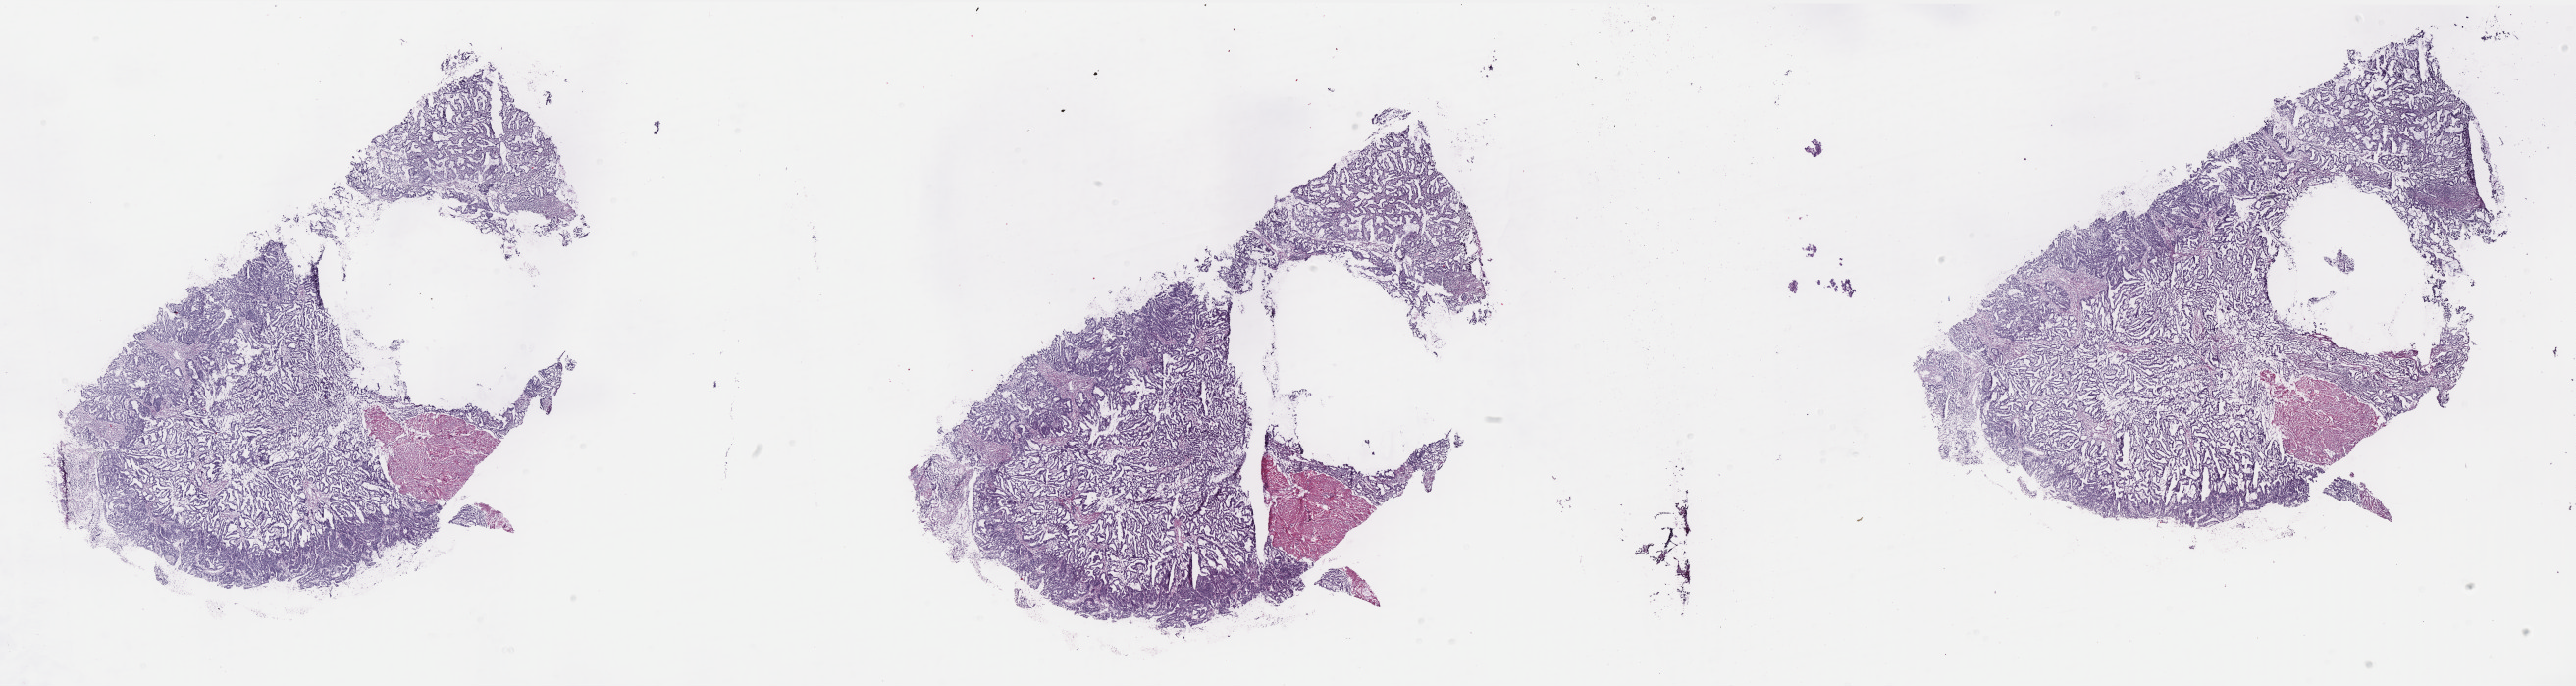
H&E whole-slide image, low-resolution overview of the scanned area, about 42.1 x 11.2 mm (slide scanned at 40x); frozen section; uterus, primary tumour sample. Patient: female, age at initial diagnosis 53 years. Histologic grade: G1 (well differentiated). Slide review estimates, as recorded: tumour cells 90%, tumour nuclei 85%, normal cells 10%, stromal cells 0%, necrosis 0%. Inflammatory infiltration, as recorded: lymphocyte infiltration 1%, monocyte infiltration 0%, neutrophil infiltration 0%.
• histologic diagnosis: Endometrioid adenocarcinoma, NOS (endometrium)
• FIGO stage: IA